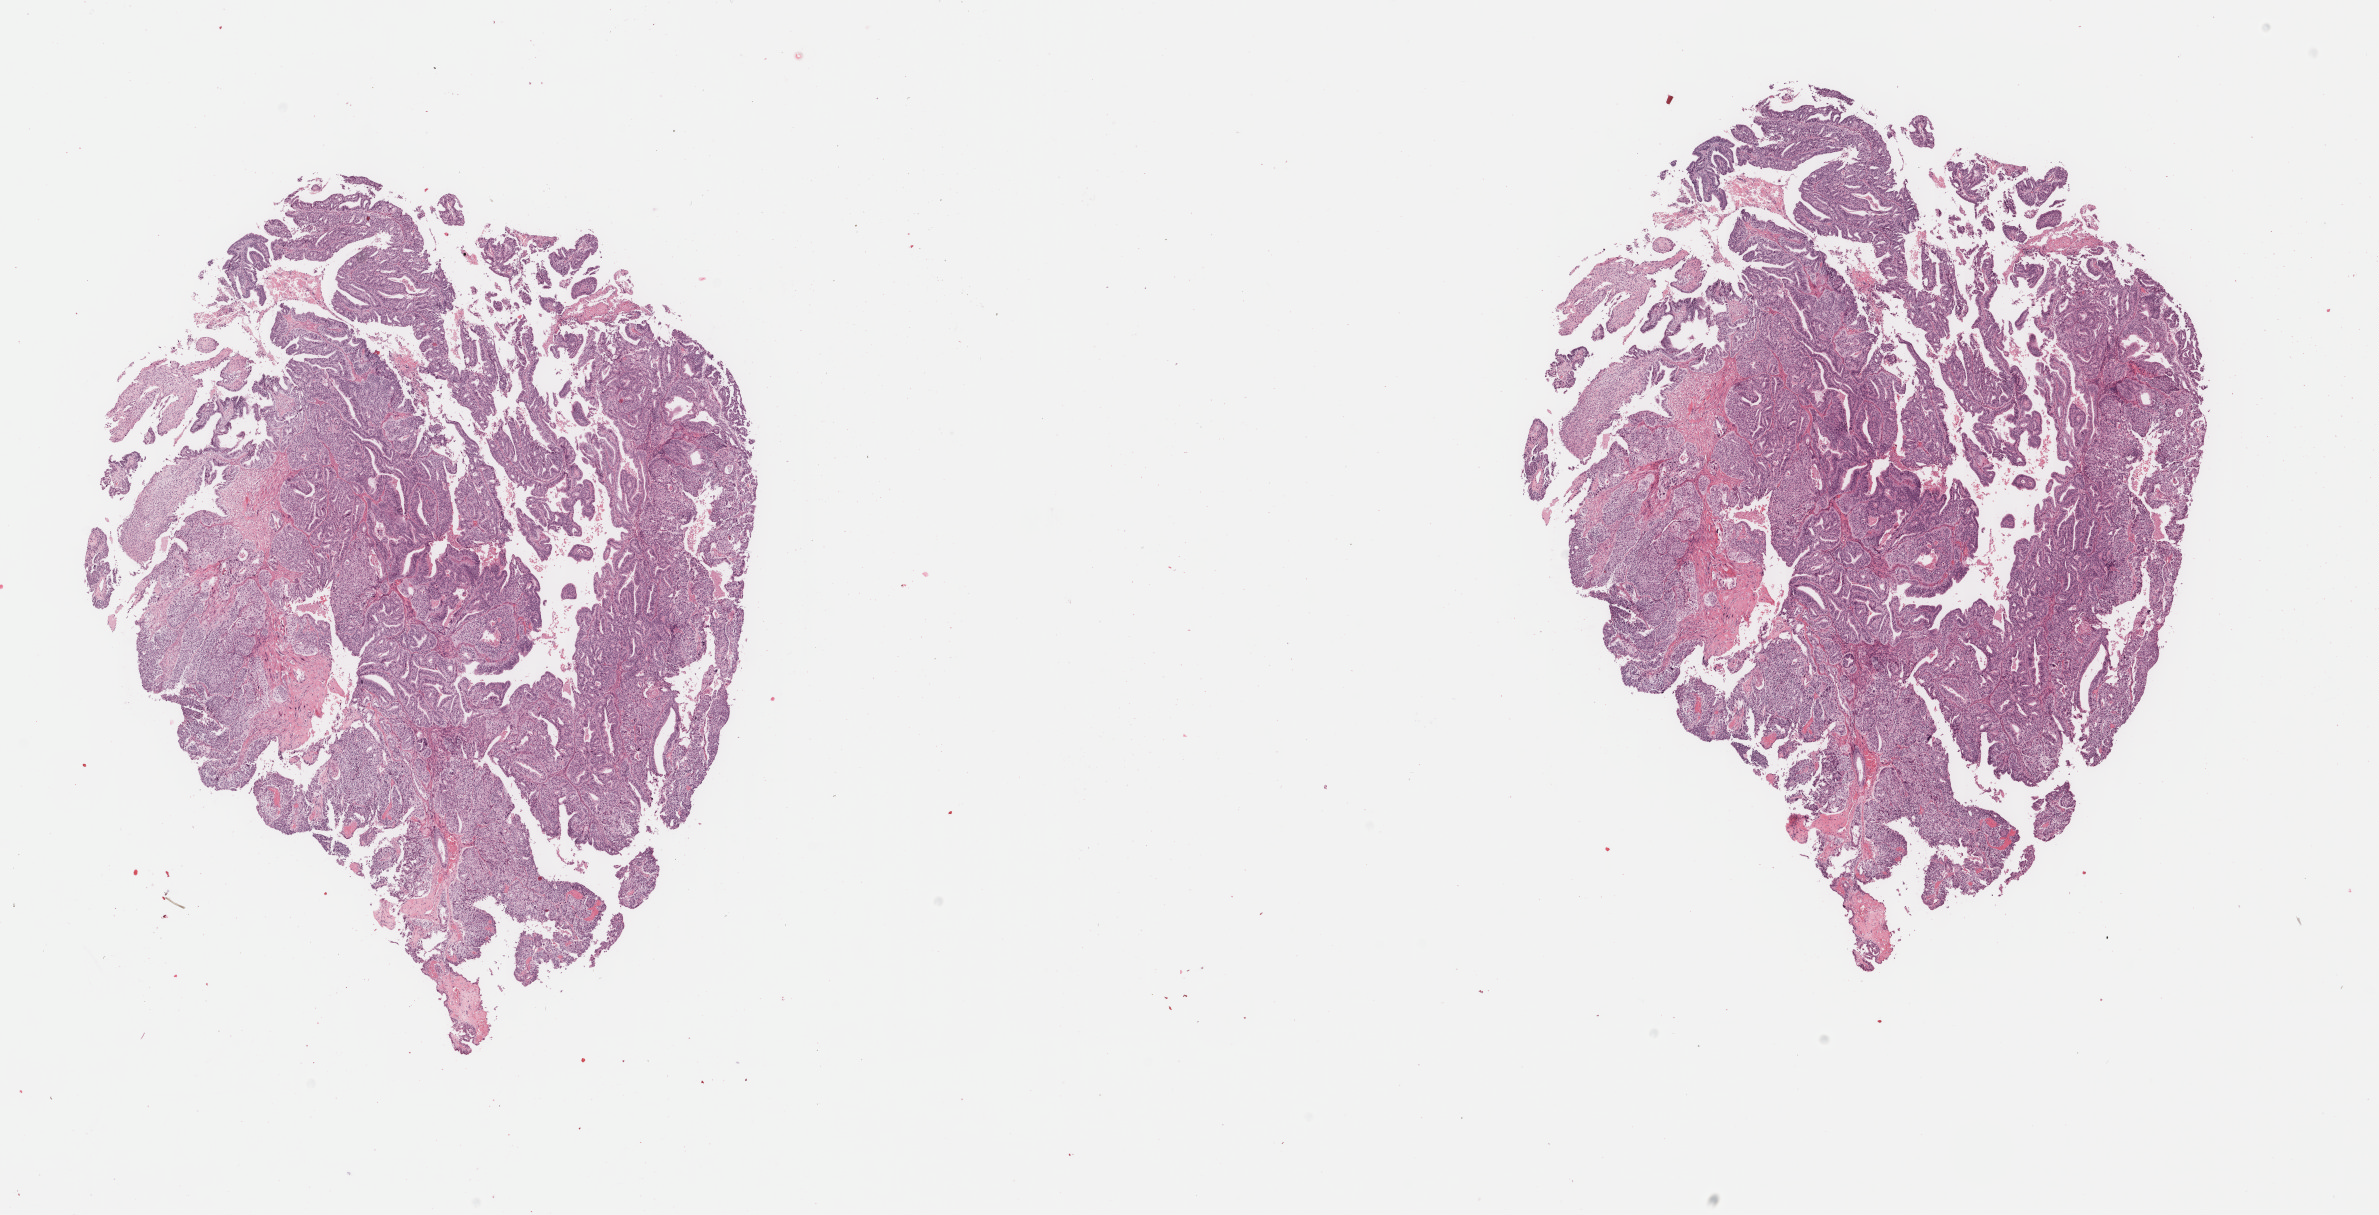
H&E whole-slide image — low-resolution overview of the scanned area, about 18.9 x 9.6 mm (slide scanned at 40x), formalin-fixed paraffin-embedded (FFPE) diagnostic section, uterus, primary tumour sample. Female patient; age at initial diagnosis 83 years. Histologic grade: G3 (poorly differentiated).
Histologic diagnosis: Endometrioid adenocarcinoma, NOS (endometrium). FIGO stage: IB.